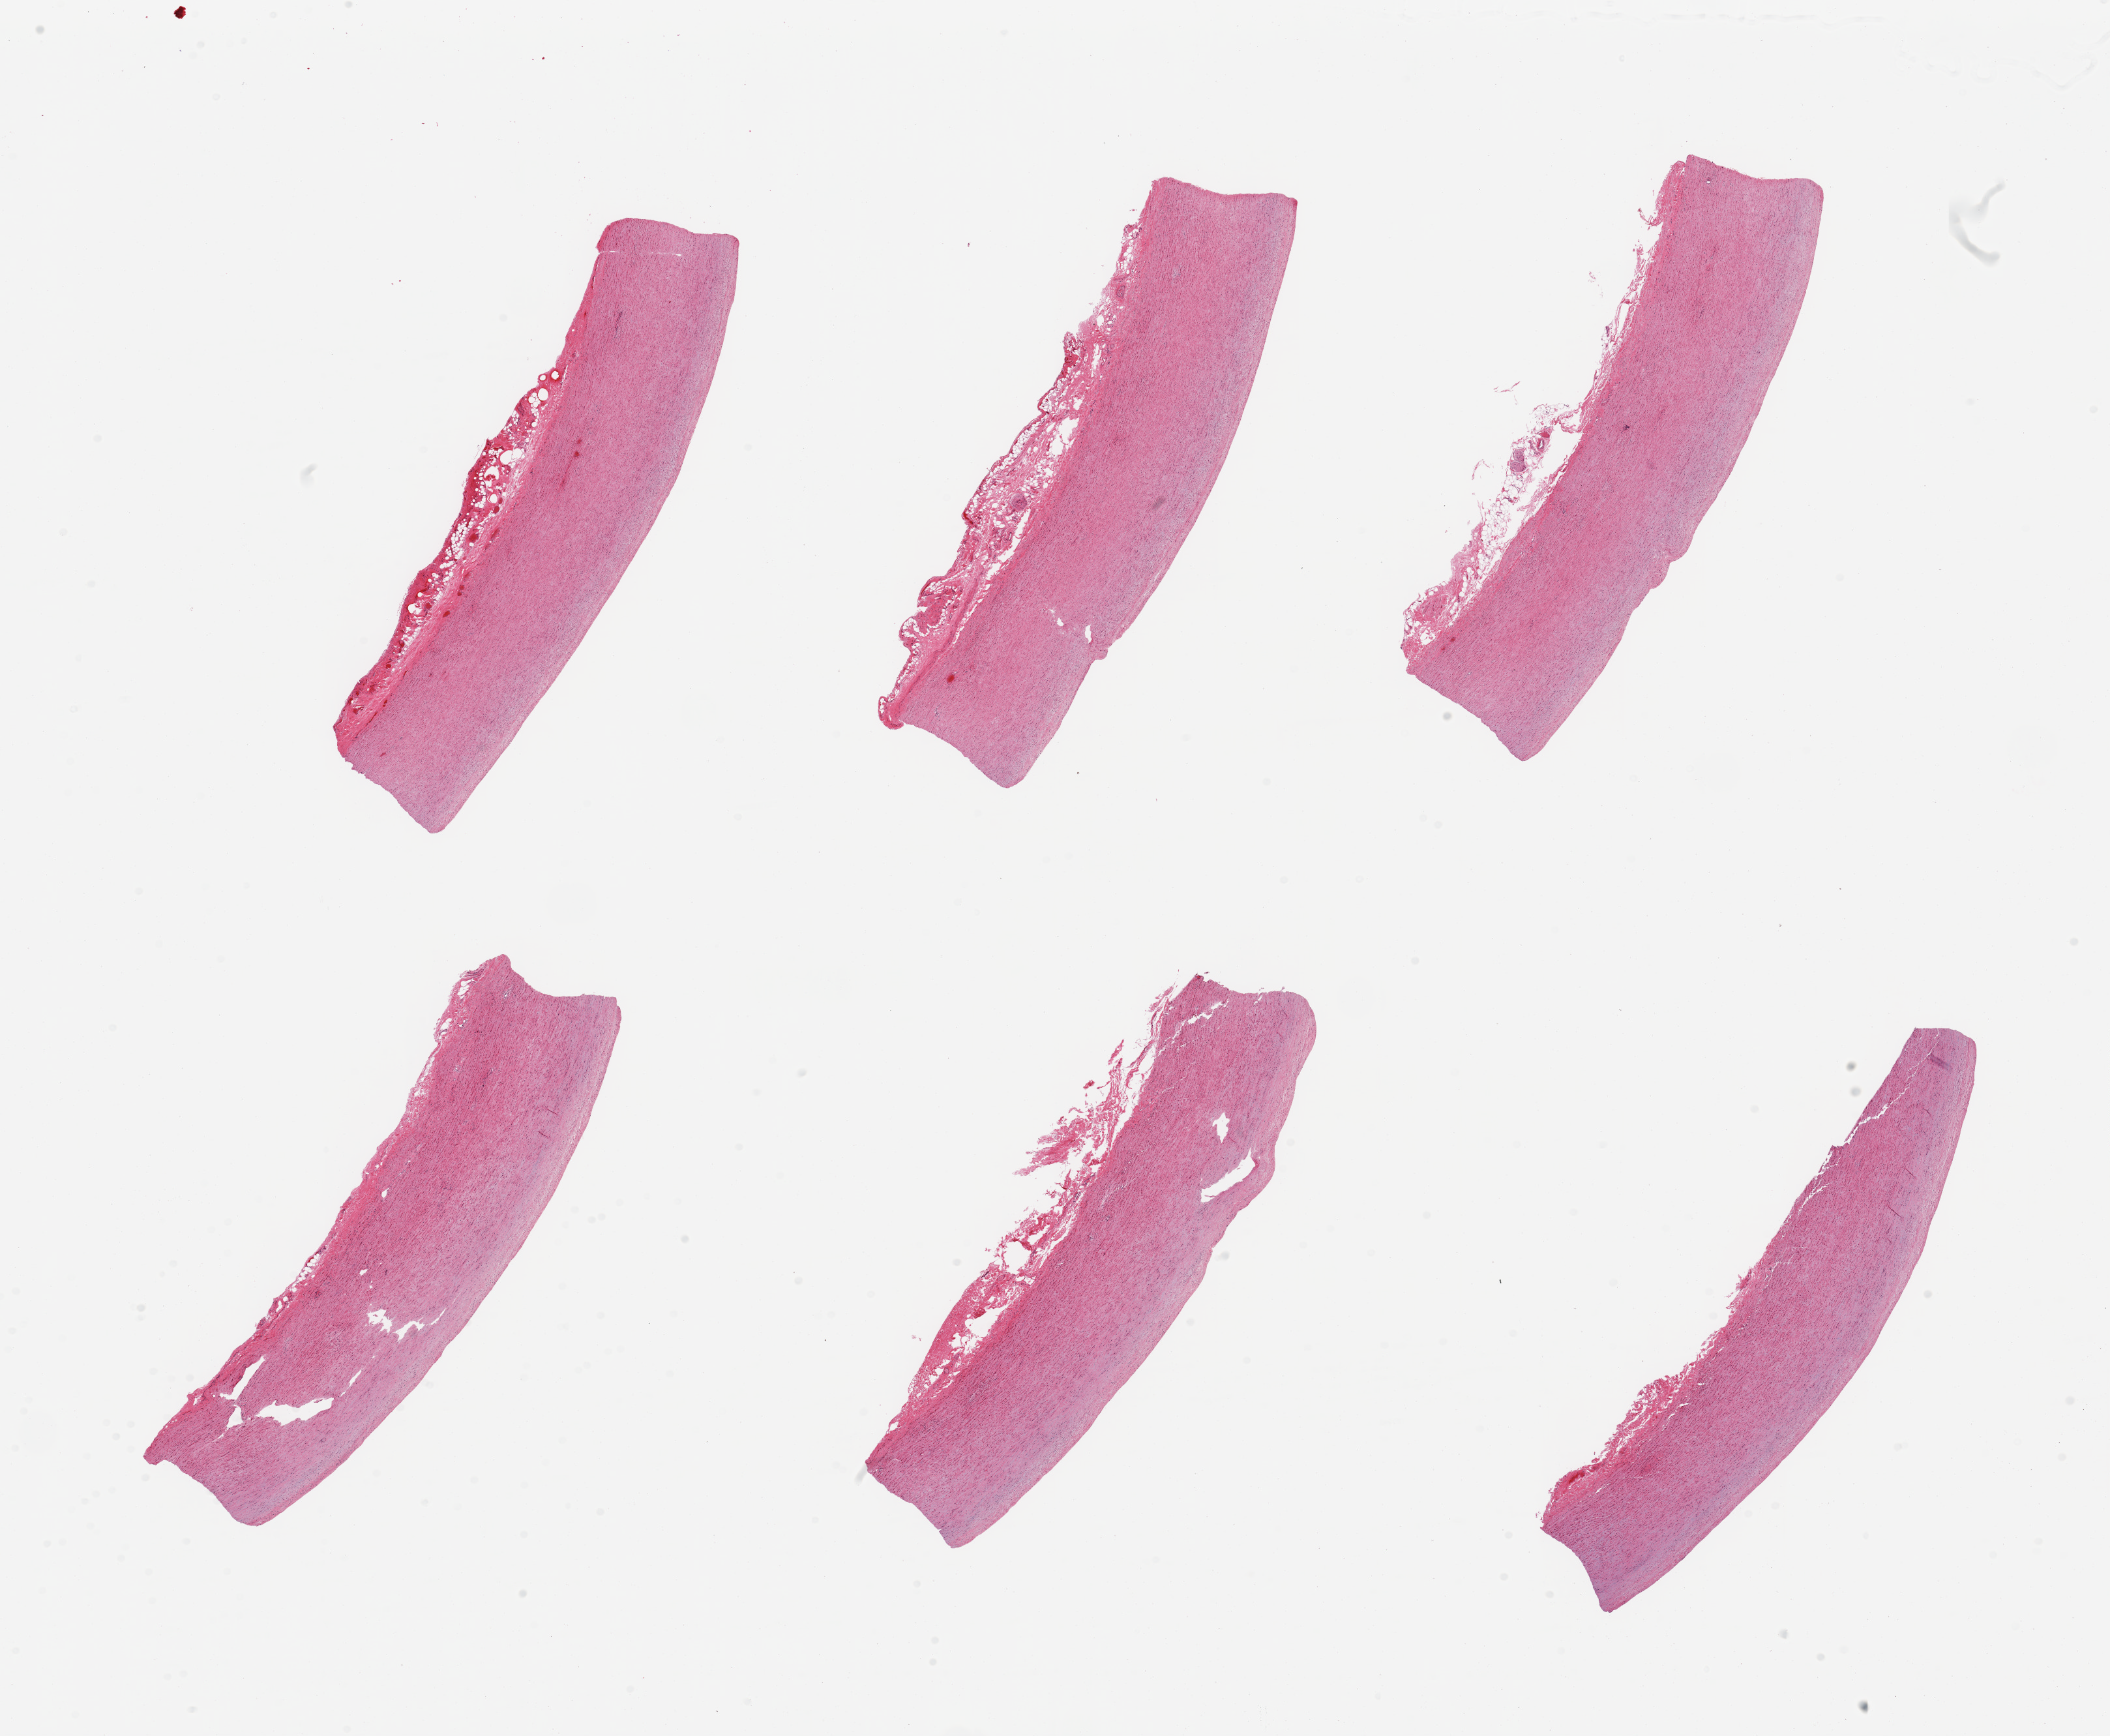
Whole-slide image, haematoxylin and eosin stain — low-resolution overview of the scanned area, about 25.6 x 21.1 mm (acquisition: 20x scan); PAXgene-fixed, paraffin-embedded tissue; sampled site (target tissue): aorta; tissue donor sample. Donor sex: male.
Pathologist's review note for this sample: 6 pieces; flat atherosclerotic plaque; some adherent congested adventitia.